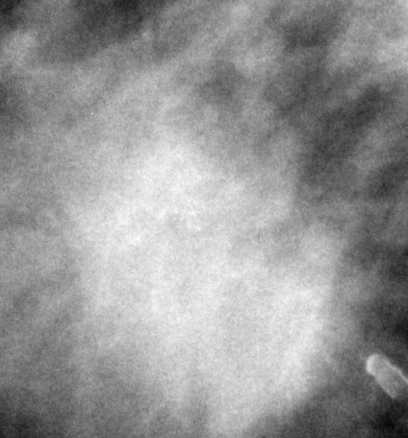
Crop from a digitized film mammogram around one marked abnormality, left breast, MLO view.
Marked abnormality: mass, shape round, margins spiculated; BI-RADS assessment category 5; subtlety rating 5 on a 1 (subtle) to 5 (obvious) scale; pathology (as recorded): malignant.